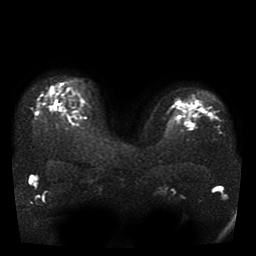
Breast MRI, one axial slice; slice 29 of 41 in the series (ordered by position); diffusion-weighted series; image 2 of 4 stored at this slice position (different b-values; order by instance number); 1.5 T; 5 mm slice thickness; 256 × 256 image matrix, field of view 330 × 330 mm. Female patient.
Outlined on this slice (expert manual segmentation):
- tumour on diffusion-weighted imaging: bounding box [x1, y1, x2, y2] px = [188, 123, 195, 126]